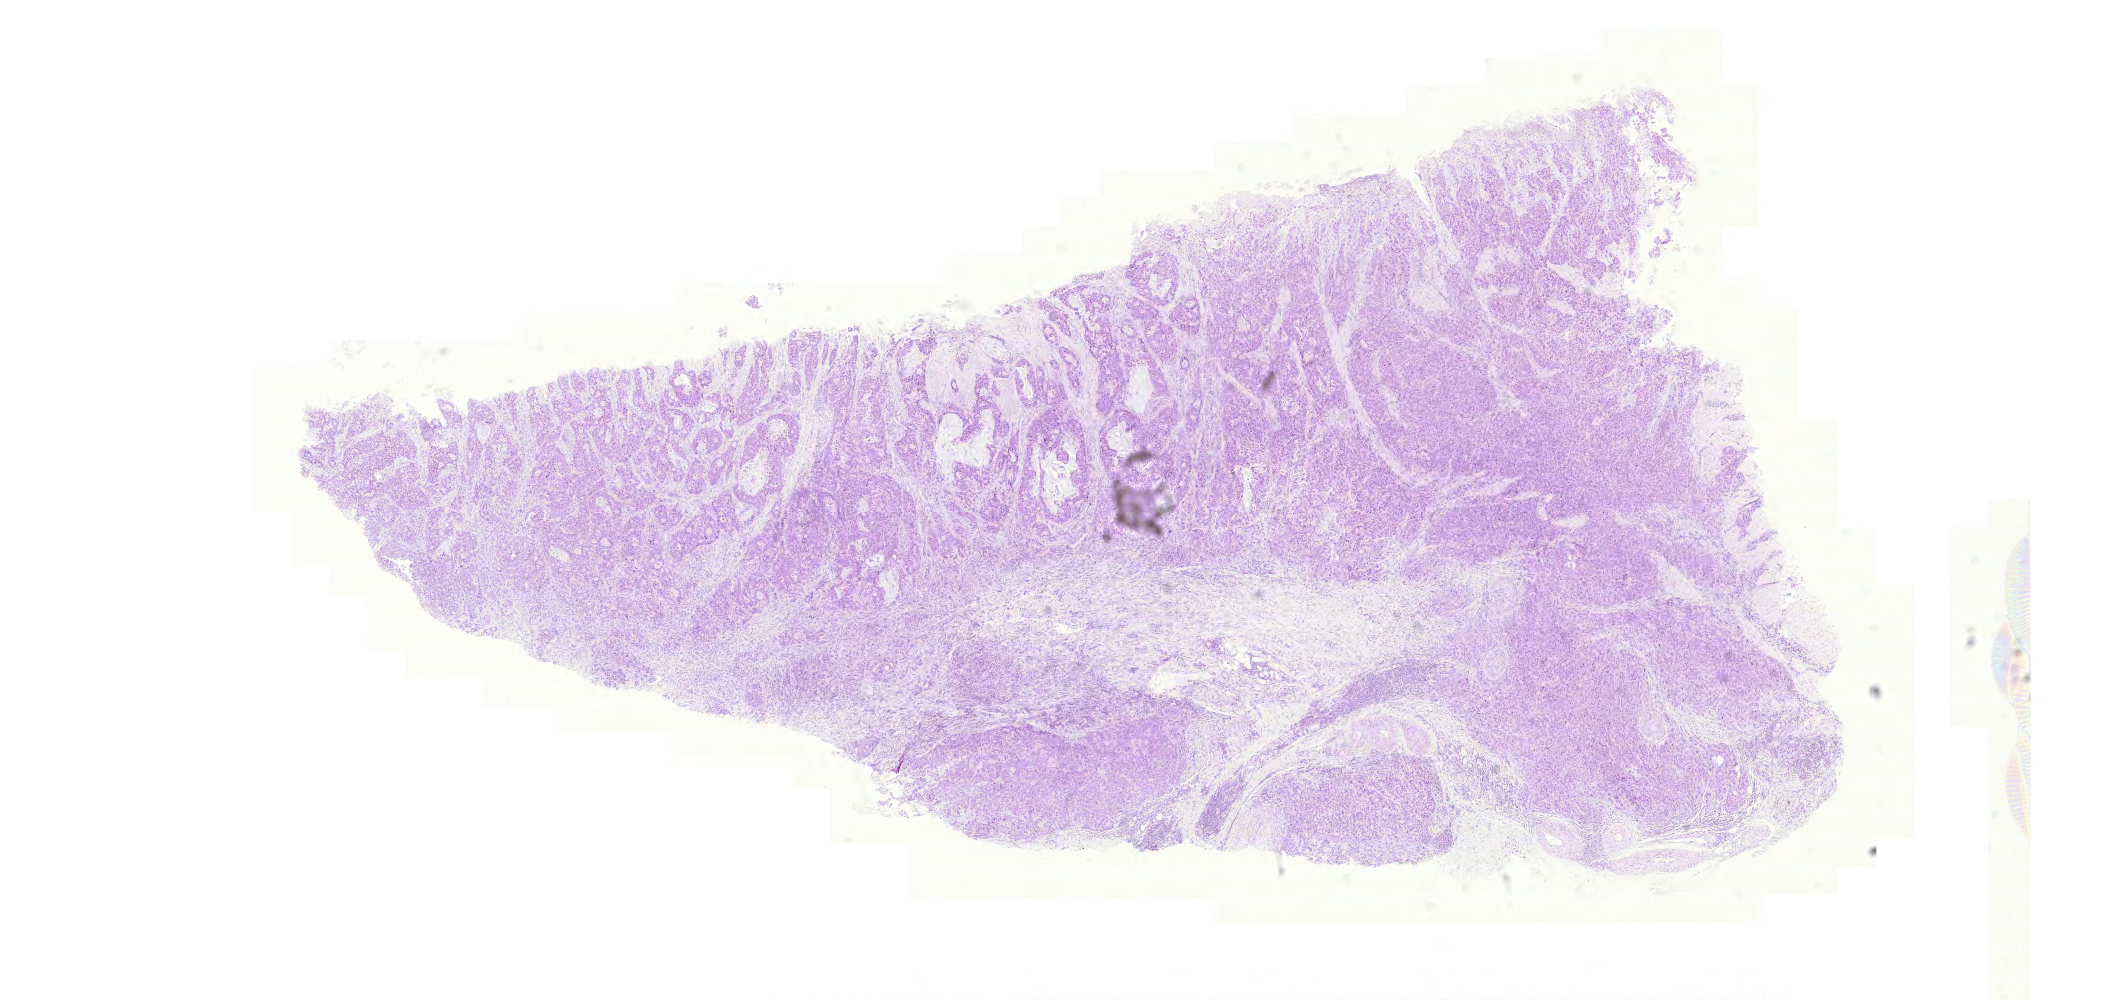
Whole-slide histology image, H&E-stained, whole scanned area (about 15.7 x 7.4 mm, from a 20x scan) shown as a low-resolution overview; FFPE section; stomach, primary tumour sample. Male, age 56 years at initial diagnosis. Histologic grade: G3 (poorly differentiated).
• pathologic diagnosis: Adenocarcinoma, intestinal type (gastric antrum)
• AJCC pathologic stage: IV (5th edition)
• TNM: T4 N2 M0
• lymph nodes positive (case pathology): 14 of 35 examined